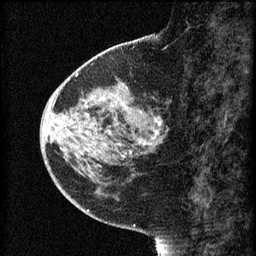
Breast MRI (dynamic contrast-enhanced), one sagittal slice; position 25 of 60 along the scan axis; 3 images stored at this slice position (order not interpretable as contrast timing); 1.5 T; TE 4.2 ms, TR 8.2 ms; 2 mm slice thickness; 256 × 256 image matrix, field of view 180 × 180 mm. Female patient, age 44 years.
Outlined on this slice (semi-automatic segmentation, software-assisted and operator-edited):
- analysis volume of interest (the breast-tissue region the enhancement analysis was run in; not a lesion): bounding box (x1, y1, x2, y2) in pixels: (73, 82, 169, 165)
- tumour enhancement mask (voxels above the 70 % enhancement threshold inside the analysis volume of interest): (123, 102, 162, 159)